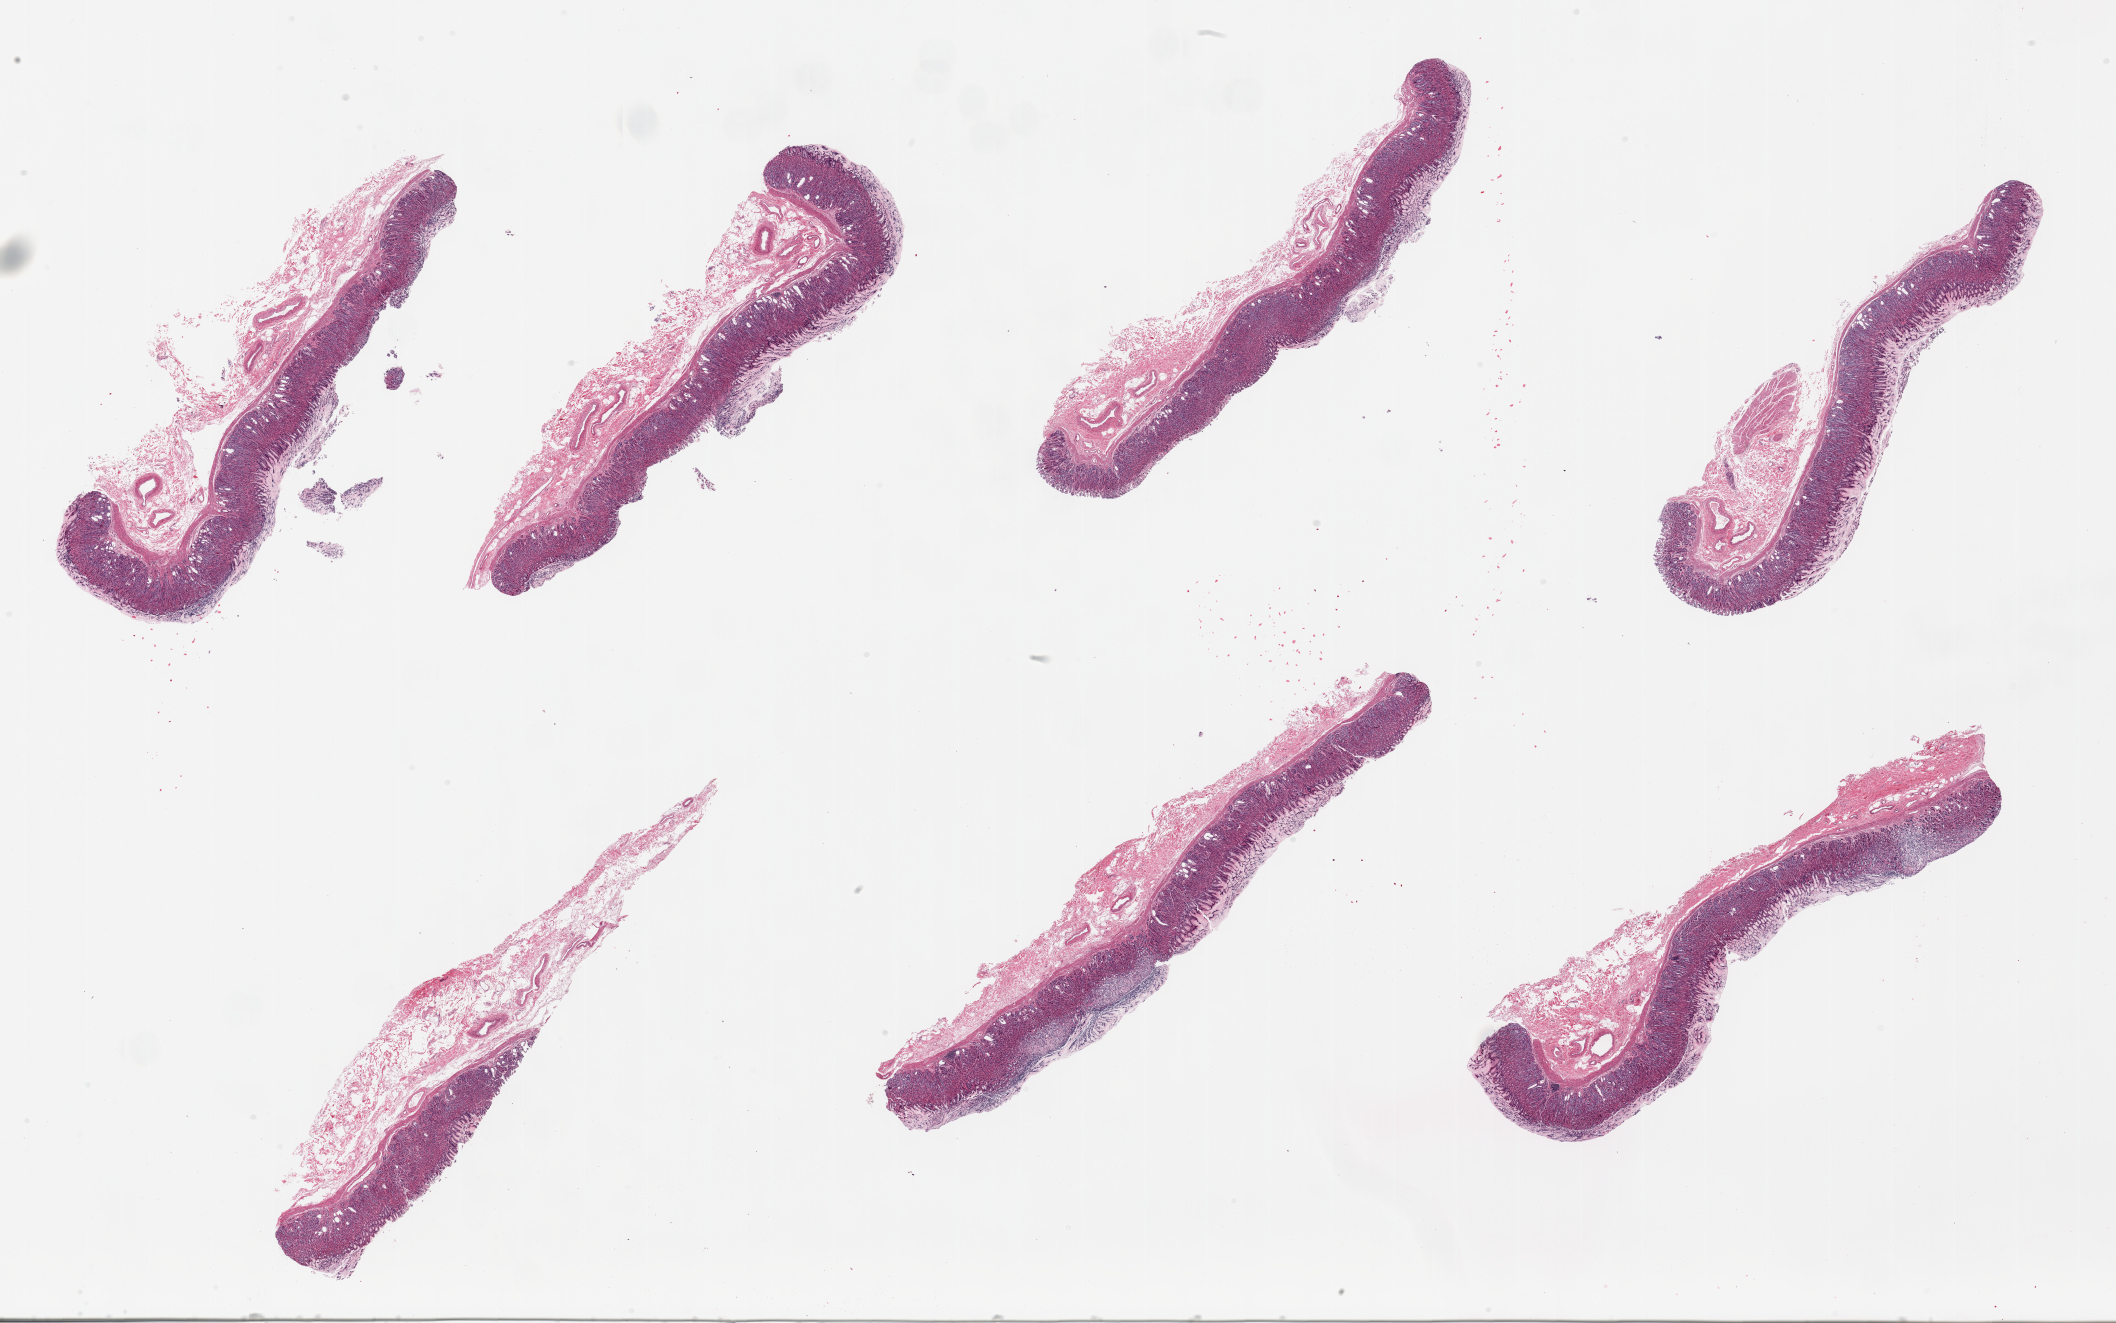
H&E whole-slide image, shown as a low-resolution overview of the whole scanned area (about 33.5 x 20.9 mm). PAXgene-fixed paraffin-embedded (PFPE) section. Target tissue: stomach. Donor tissue sample. Donor sex: male.
• reviewer comment on this tissue sample: 6 pieces, generally well preserved mucosa up to ~1mm, 60-90% thickness; Several foci of moderate-advance autolysis